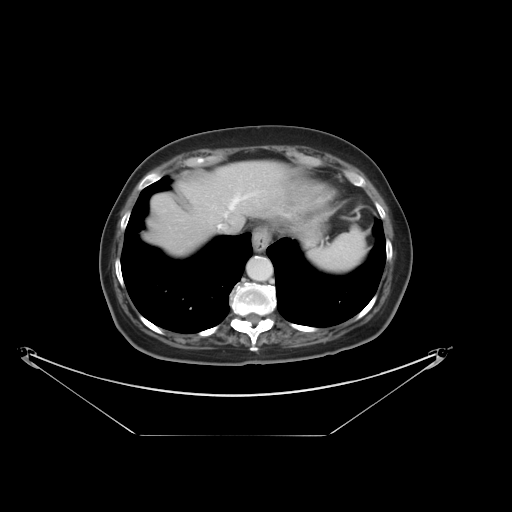
Contrast-enhanced abdominal CT, one axial slice. Position 31 of 36 along the scan axis. Intravenous contrast given. Soft-tissue window (W 400 / L 40 HU). 512 × 512 image matrix, field of view 500 × 500 mm. Female patient, age 70 years. From the clinical record (not read from this slice): diagnosis: colorectal cancer liver metastases, imaged before liver resection; multiple liver metastases: no; largest metastasis: 2.5 cm; disease in both lobes: no.
Structures marked on this image (outlined manually by an expert reader):
- hepatic veins: box from (x=211, y=196) to (x=248, y=229) px
- liver: (x=145, y=162)–(x=287, y=257)
- planned liver remnant (the part of the liver to remain after resection): (x=145, y=162)–(x=287, y=257)